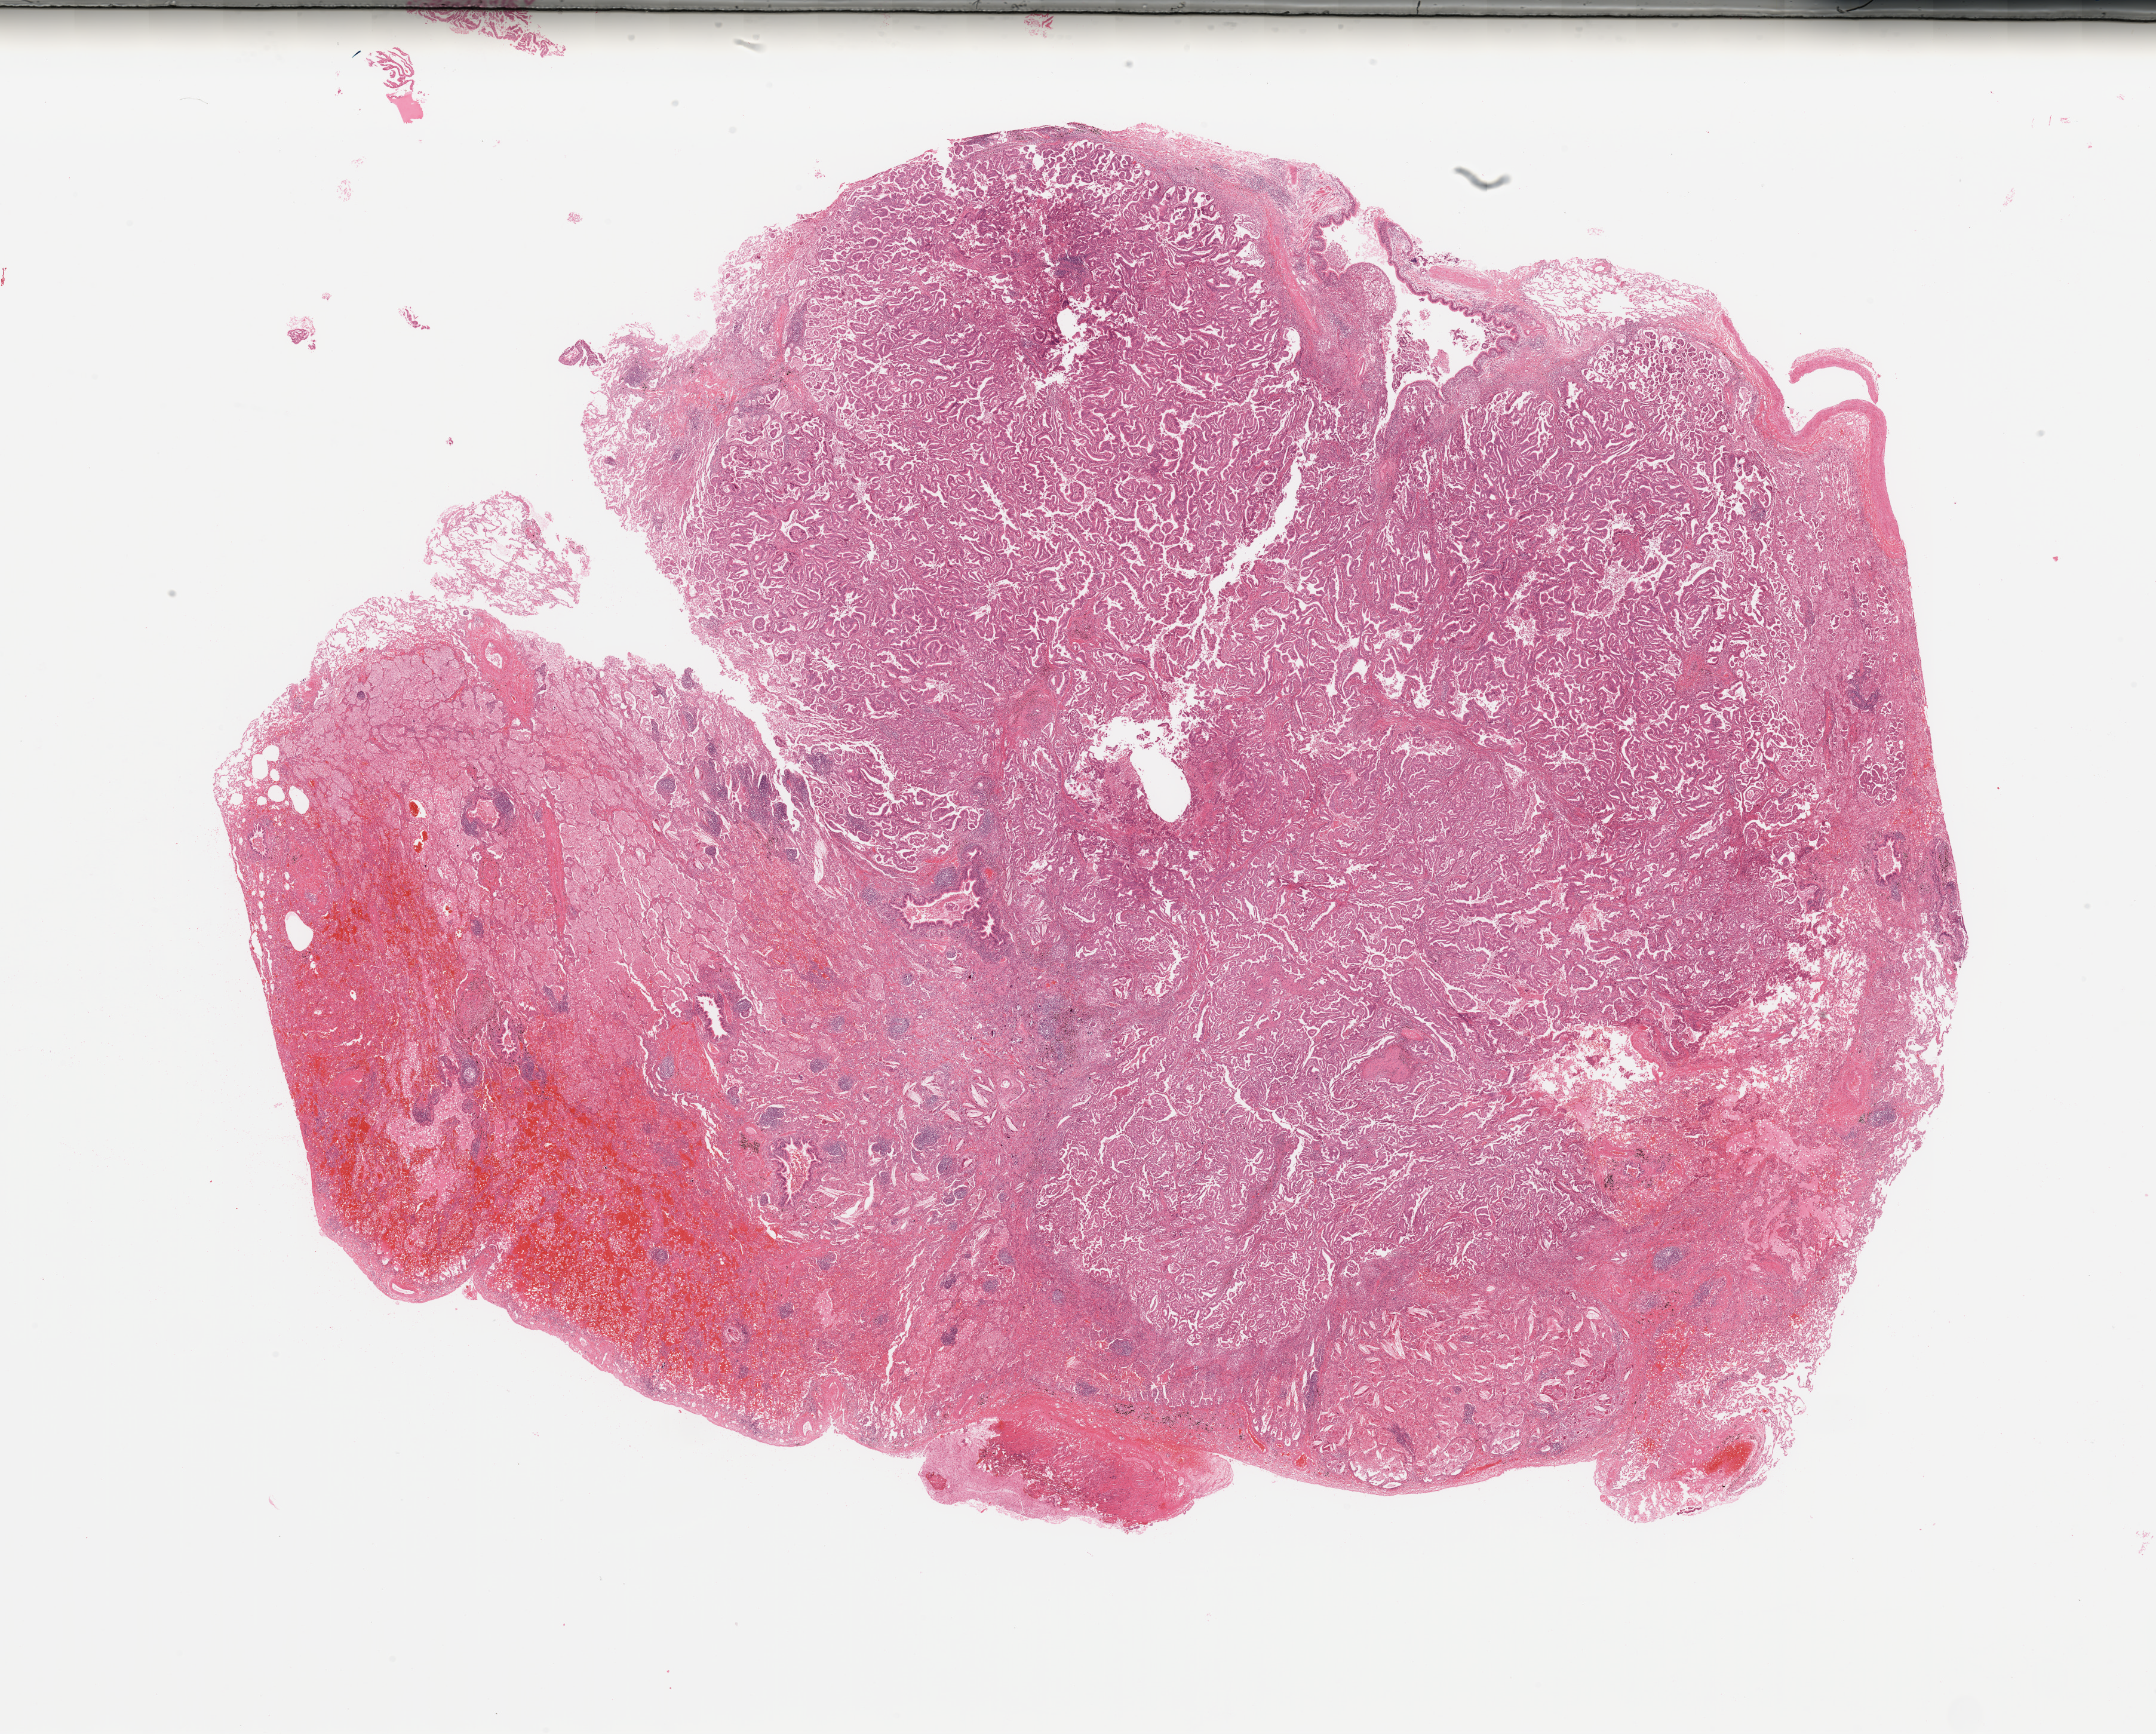
Digitized H&E-stained tissue section (whole slide) — a low-resolution overview of the entire scanned area, about 28.5 x 23.0 mm (from a 20x scan); tumour tissue sample, sampled site: lung. Patient: male, age 67 years. Histologic grade: G2 (moderately differentiated). Pathologist review of this section (percent, as recorded): tumour nuclei 65%, necrosis 2%.
Diagnosis: Adenocarcinoma, NOS. AJCC pathologic stage: IIIA.